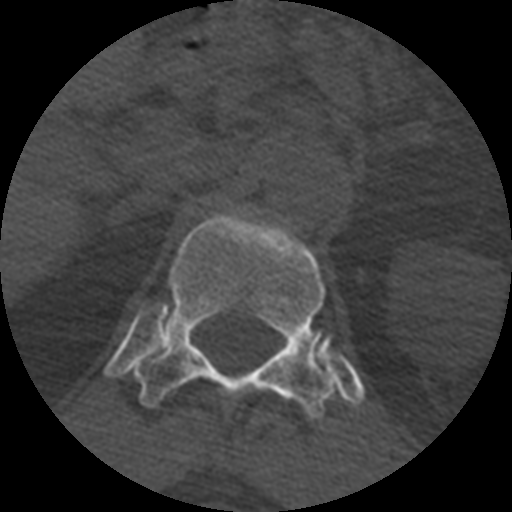
CT including the spine, one axial slice; position 386 of 399 along the scan axis; 120 kVp; bone window (W 1800 / L 400 HU); 512 × 512 image matrix. Patient age 71 years. From the clinical record (not read from this slice): primary cancer: prostate.
Structures marked on this image (semi-automatically segmented with operator editing):
- T12 vertebra: box from (x=134, y=211) to (x=336, y=418) px